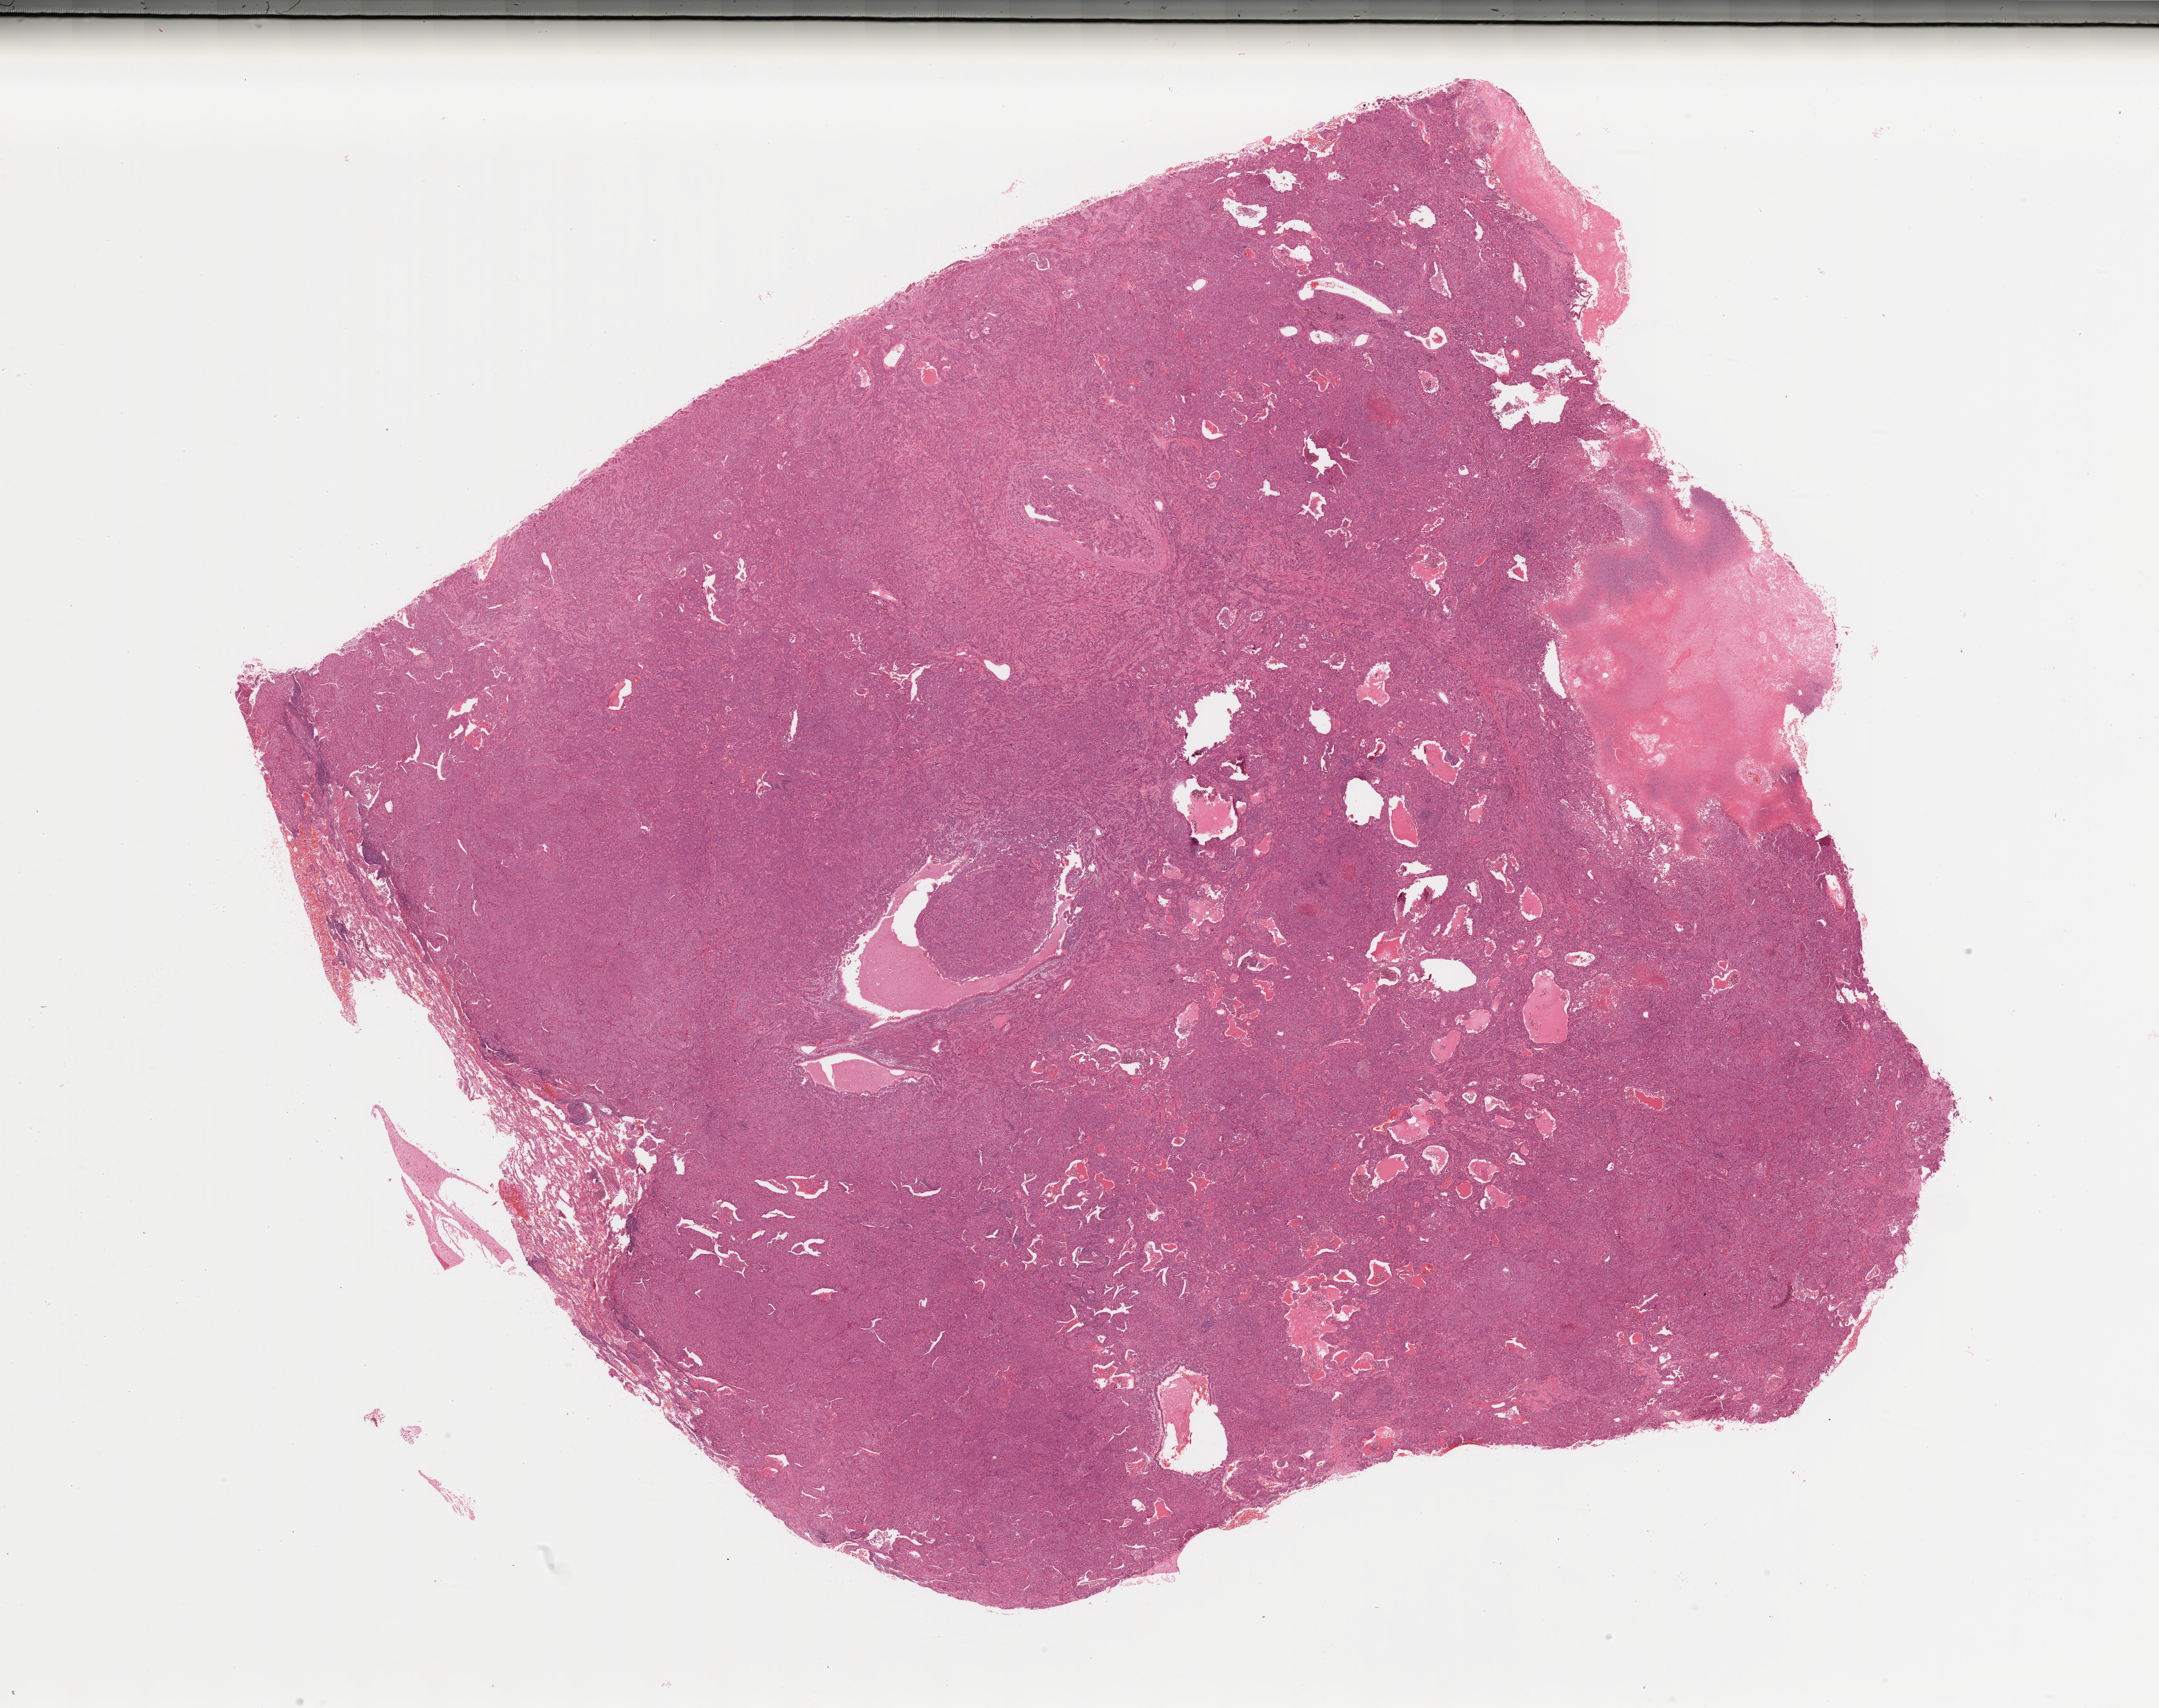
Whole-slide histology image, H&E — whole scanned area (about 29.5 x 23.4 mm, acquisition: 20x scan) shown as a low-resolution overview. Lung, tissue type not recorded.
Patient diagnosis (cohort enrolment): lung adenocarcinoma (lung).